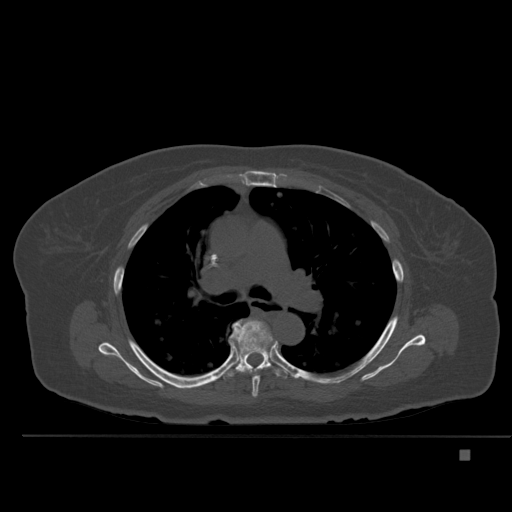
CT including the spine, one axial slice; position 346 of 477 along the scan axis; bone window (W 1800 / L 400 HU); 512 × 512 image matrix, field of view 422 × 422 mm. Patient: female, 74 years. From the clinical record (not read from this slice): primary cancer: colon.
Annotated regions visible in this slice (semi-automatically segmented with operator editing):
- T5 vertebra: bounding box (x1, y1, x2, y2) in pixels: (241, 344, 274, 399)
- T6 vertebra: (222, 319, 289, 379)